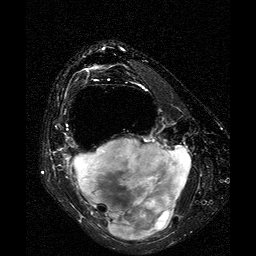
MRI of an extremity soft-tissue mass, one axial slice; position 16 of 25 along the scan axis; T2-weighted fat-saturated; 256 × 256 image matrix, field of view 160 × 160 mm. Female patient. From the clinical record (not read from this slice): histological type: liposarcoma; site of the primary tumour: right thigh.
Structures marked on this image (manually delineated by an expert):
- gross tumour volume (mass): box from (x=70, y=139) to (x=190, y=241) px